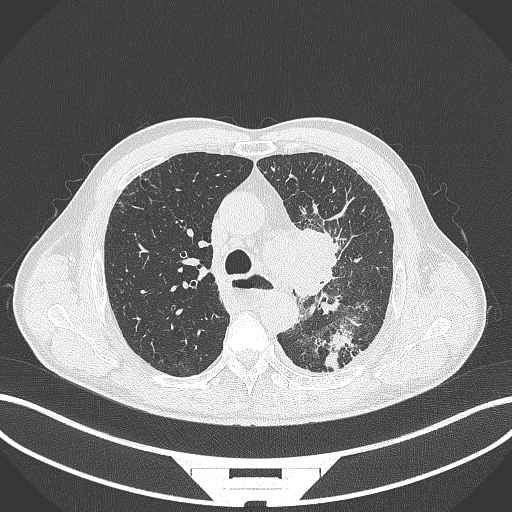
Chest CT, one axial slice. Position 264 of 411 along the scan axis. Reconstruction kernel B70f. Lung window (W 1500 / L -600 HU). 512 × 512 image matrix, field of view 400 × 400 mm. Male patient, age 57 years. Case-level facts recorded for this patient, not image findings: clinical TNM (as recorded): T2a N1 M0.
Annotated regions visible in this slice (rectangle marked by the reading radiologist):
- lung tumour (recorded histology: squamous cell carcinoma): bounding box [x1, y1, x2, y2] px = [293, 222, 350, 300]